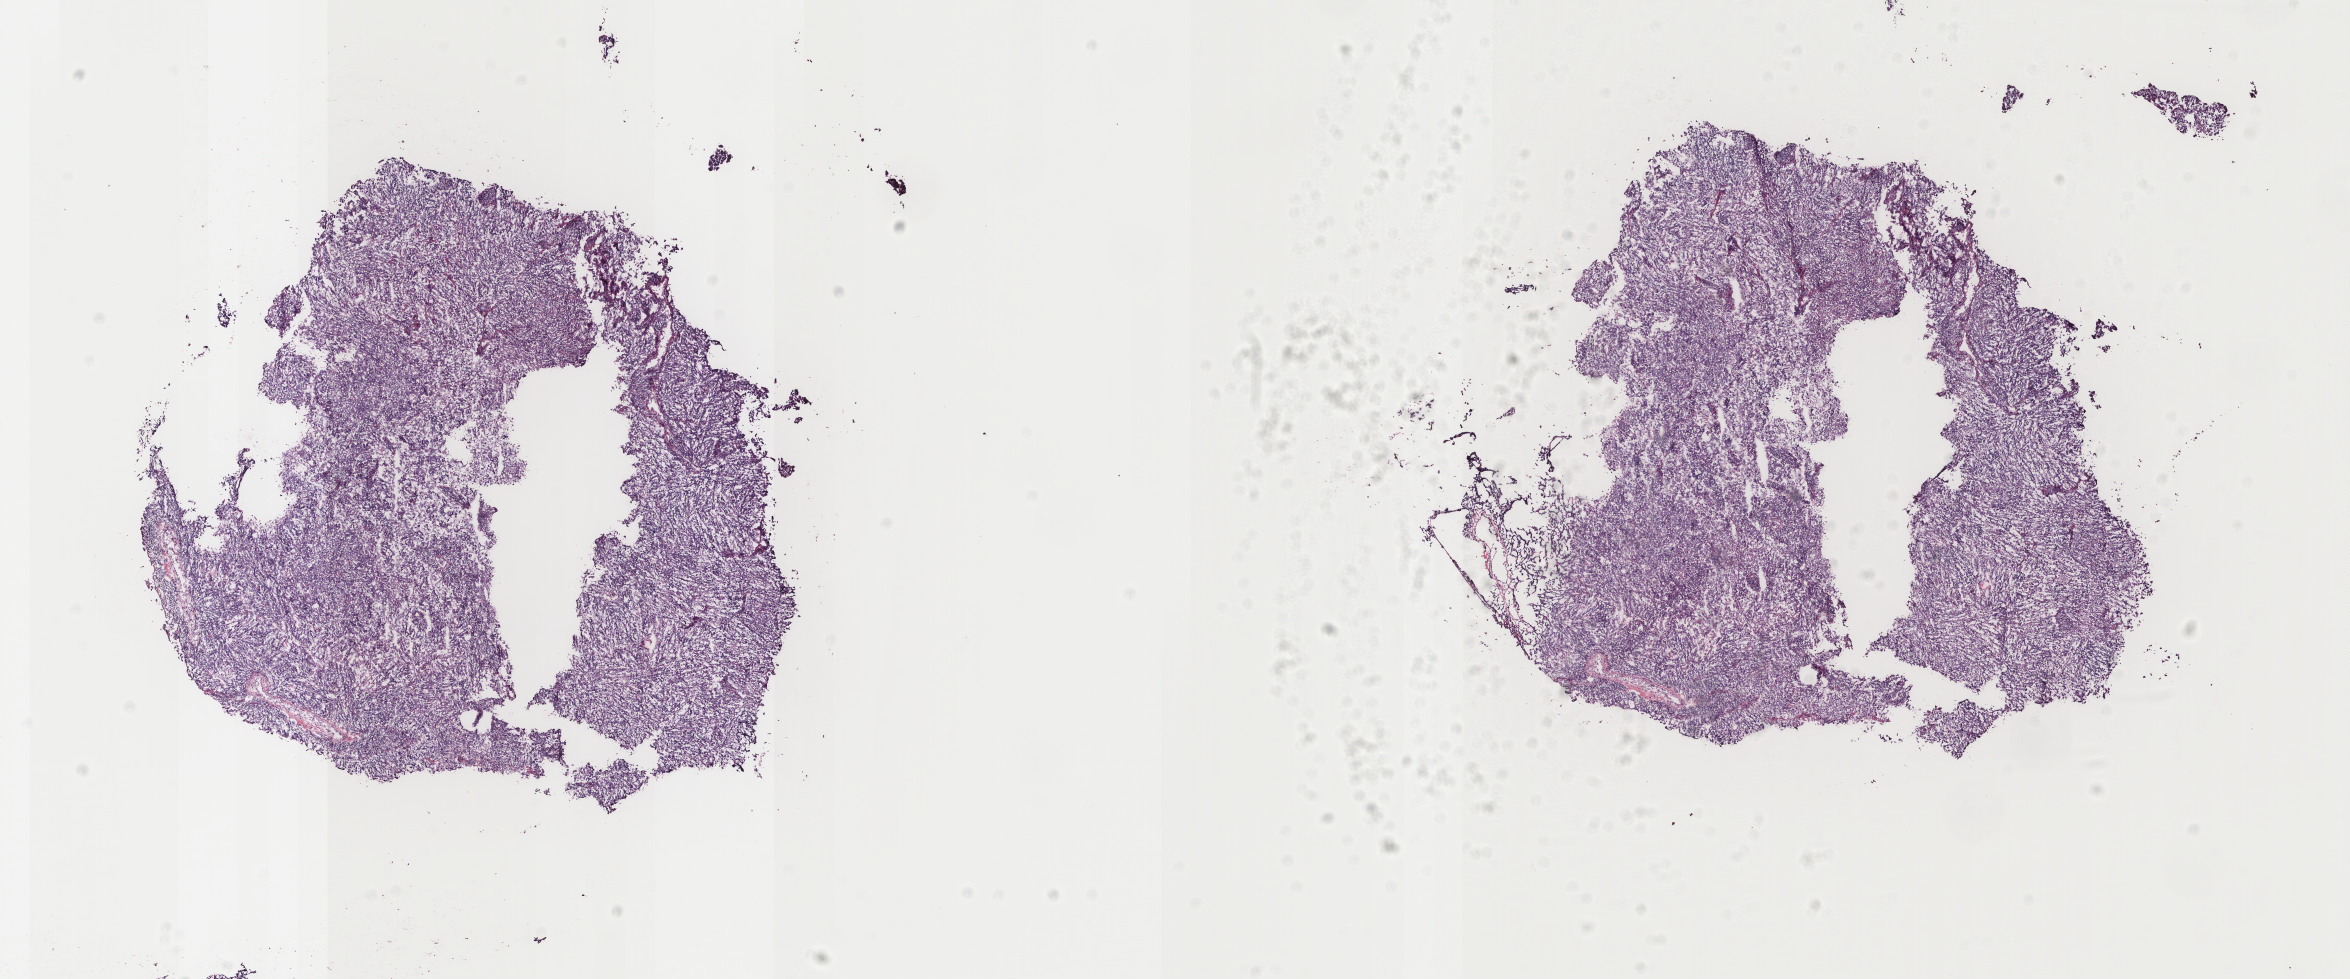
Whole-slide histology image, Hematoxylin and eosin (H&E) stained, whole scanned area (about 18.7 x 7.8 mm) shown as a low-resolution overview. Frozen section from the top of the tissue portion. Uterus, primary tumour sample. Female patient; age at initial diagnosis 84 years. Histologic grade: G3 (poorly differentiated). Slide review estimates, as recorded: tumour cells 93%, tumour nuclei 92%, normal cells 0%, stromal cells 5%, necrosis 2%. Inflammatory infiltration, as recorded: lymphocyte infiltration 3%, monocyte infiltration 1%, neutrophil infiltration 0%.
FIGO stage: IC. Histologic diagnosis: Endometrioid adenocarcinoma, NOS (endometrium).